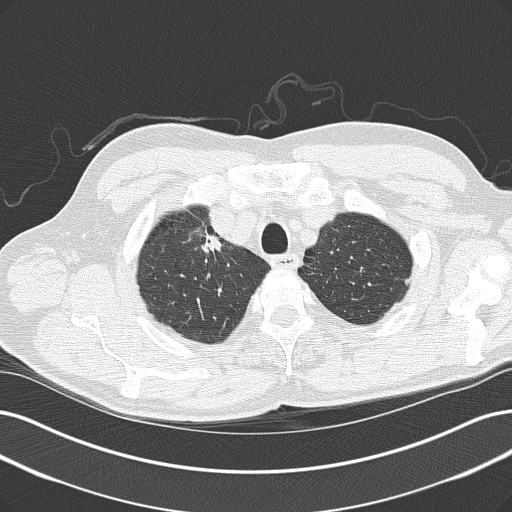
Axial slice from a low-dose chest CT screening exam, first (baseline) screen, lung window (W 1500 / L -600 HU), lung (sharp) reconstruction kernel (B50f), 120 kVp, slice 26 of 152 in the series, 512 × 512 image matrix, field of view 365 × 365 mm. Male, age 61 years at enrolment. Current smoker at enrolment.
Expert reader's lesion annotation, bounding box <191,225,245,271> (left, top, right, bottom; pixels). The screening reader recorded 2 non-calcified nodules or masses ≥4 mm on this exam (right upper lobe, right upper lobe); which of them this box marks is not recorded. Official screen result: positive, change unspecified: nodule(s) >= 4 mm or enlarging nodule(s), mass(es), or other non-specific abnormalities suspicious for lung cancer. Participant outcome: lung cancer diagnosed 54 days after this screen — adenocarcinoma, NOS, right upper lobe, poorly differentiated (G3), stage IIIB (AJCC 6th edition).